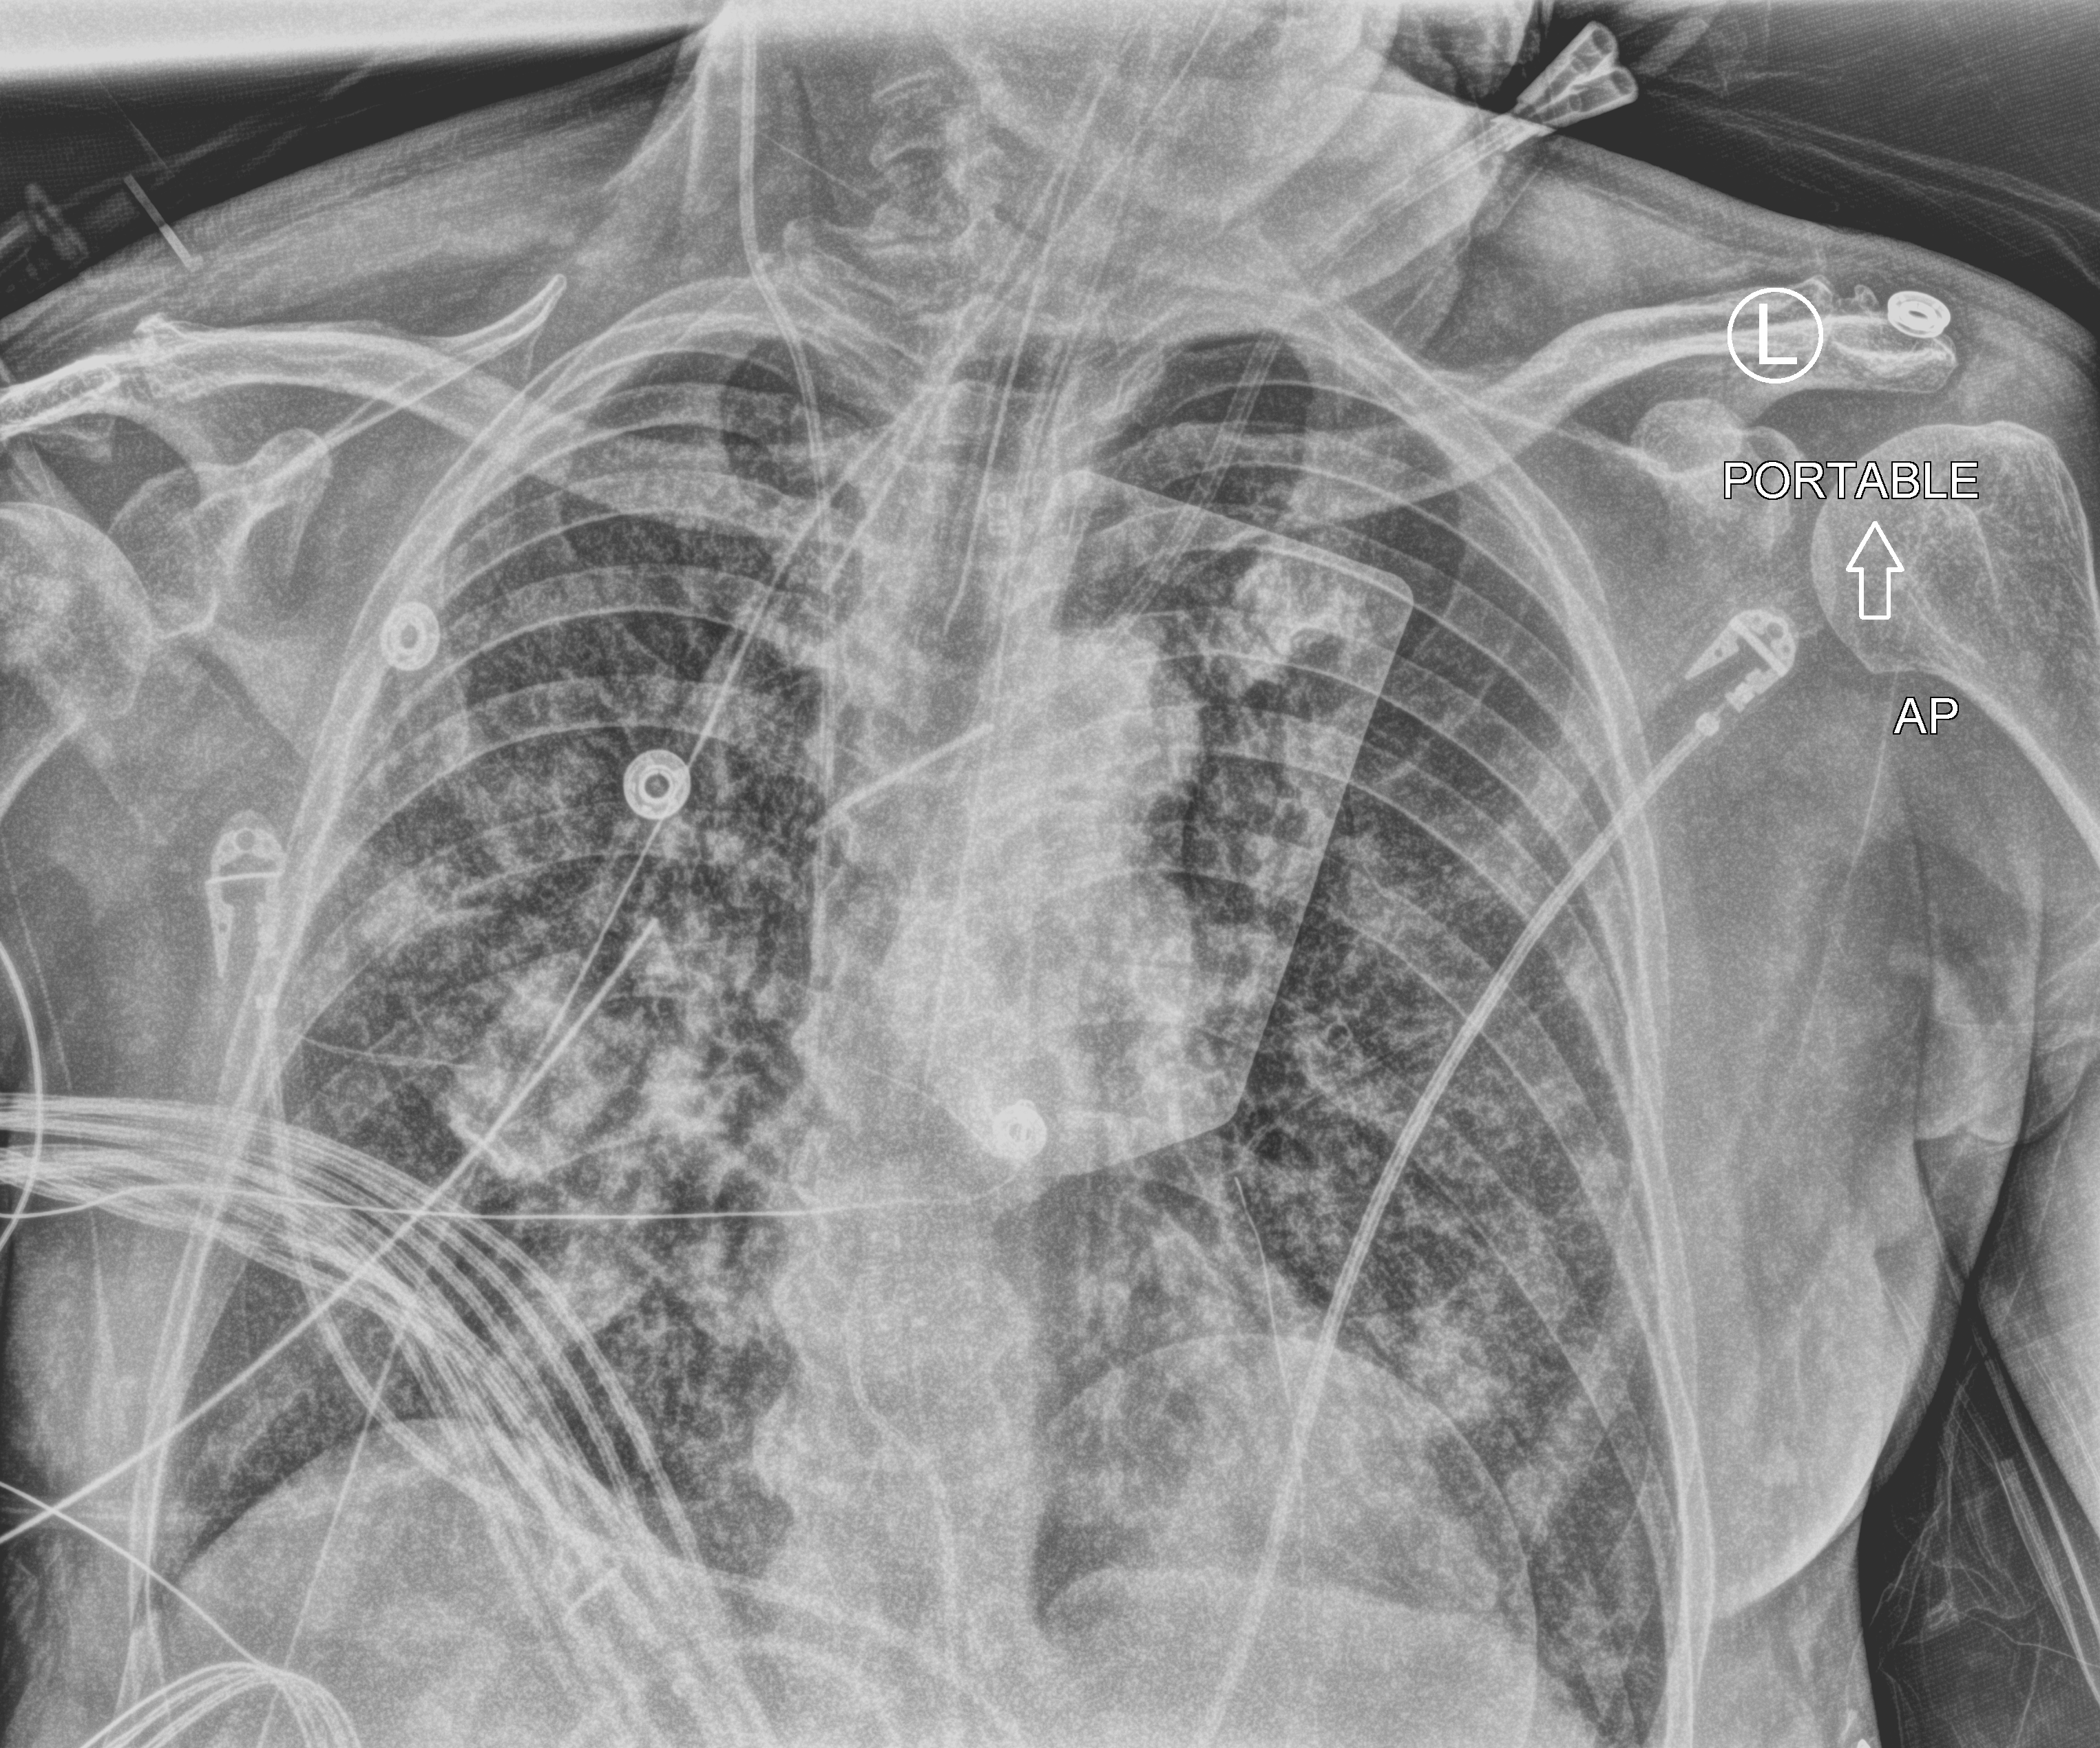
Portable chest radiograph. Male patient hospitalised with COVID-19, age 60–74 years.
From the hospital-stay record, not from the radiograph (when in the stay this image was taken is not recorded): admitted to intensive care during this hospital stay: yes.